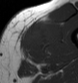
MRI of an extremity soft-tissue mass, one axial slice; MR volume resampled by the dataset authors to the PET/CT grid (not the native acquisition matrix); 3.27 mm slice thickness; 78 × 83 image matrix, field of view 76 × 81 mm. Male patient. Case-level facts recorded for this patient, not image findings: histological type: pleiomorphic leiomyosarcoma; grade: high; site of the primary tumour: left thigh.
Structures marked on this image (expert contour drawn on MRI and transferred to this co-registered scan by the dataset authors):
- gross tumour volume including surrounding oedema: bounding box [x1, y1, x2, y2] px = [18, 19, 57, 61]
- gross tumour volume (mass): [22, 26, 48, 59]